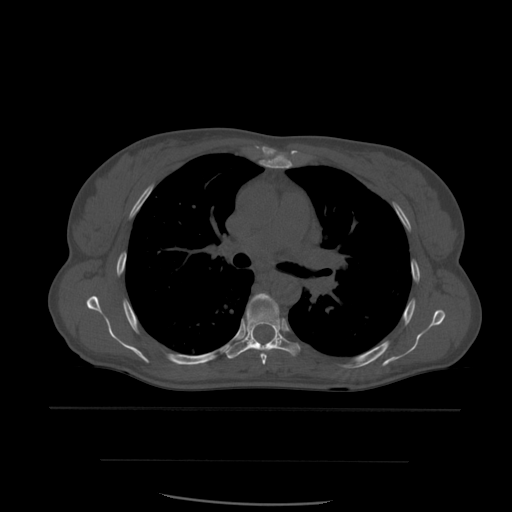
CT including the spine, one axial slice. Slice 398 of 574 in the series (ordered by position). Bone window (W 1800 / L 400 HU). 512 × 512 image matrix, field of view 392 × 392 mm. Patient age 48 years. Case-level facts recorded for this patient, not image findings: primary cancer: lung.
Structures marked on this image (semi-automatic segmentation, software-assisted and operator-edited):
- T5 vertebra: bounding box [x1, y1, x2, y2] px = [253, 294, 276, 366]
- T6 vertebra: [227, 299, 300, 359]